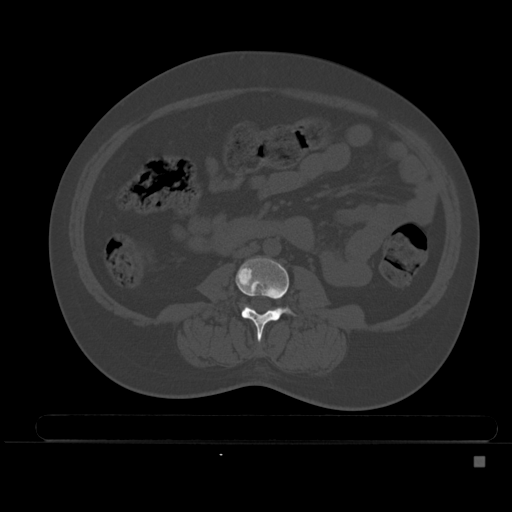
CT including the spine, one axial slice. Slice 148 of 495 in the series (ordered by position). Bone window (W 1800 / L 400 HU). 512 × 512 image matrix, field of view 404 × 404 mm. Patient: female, 33 years. Case-level facts recorded for this patient, not image findings: primary cancer: breast; vertebrae with lytic lesions (as recorded): T1.
Outlined on this slice (semi-automatically segmented with operator editing):
- L3 vertebra: box from (x=236, y=257) to (x=300, y=341) px